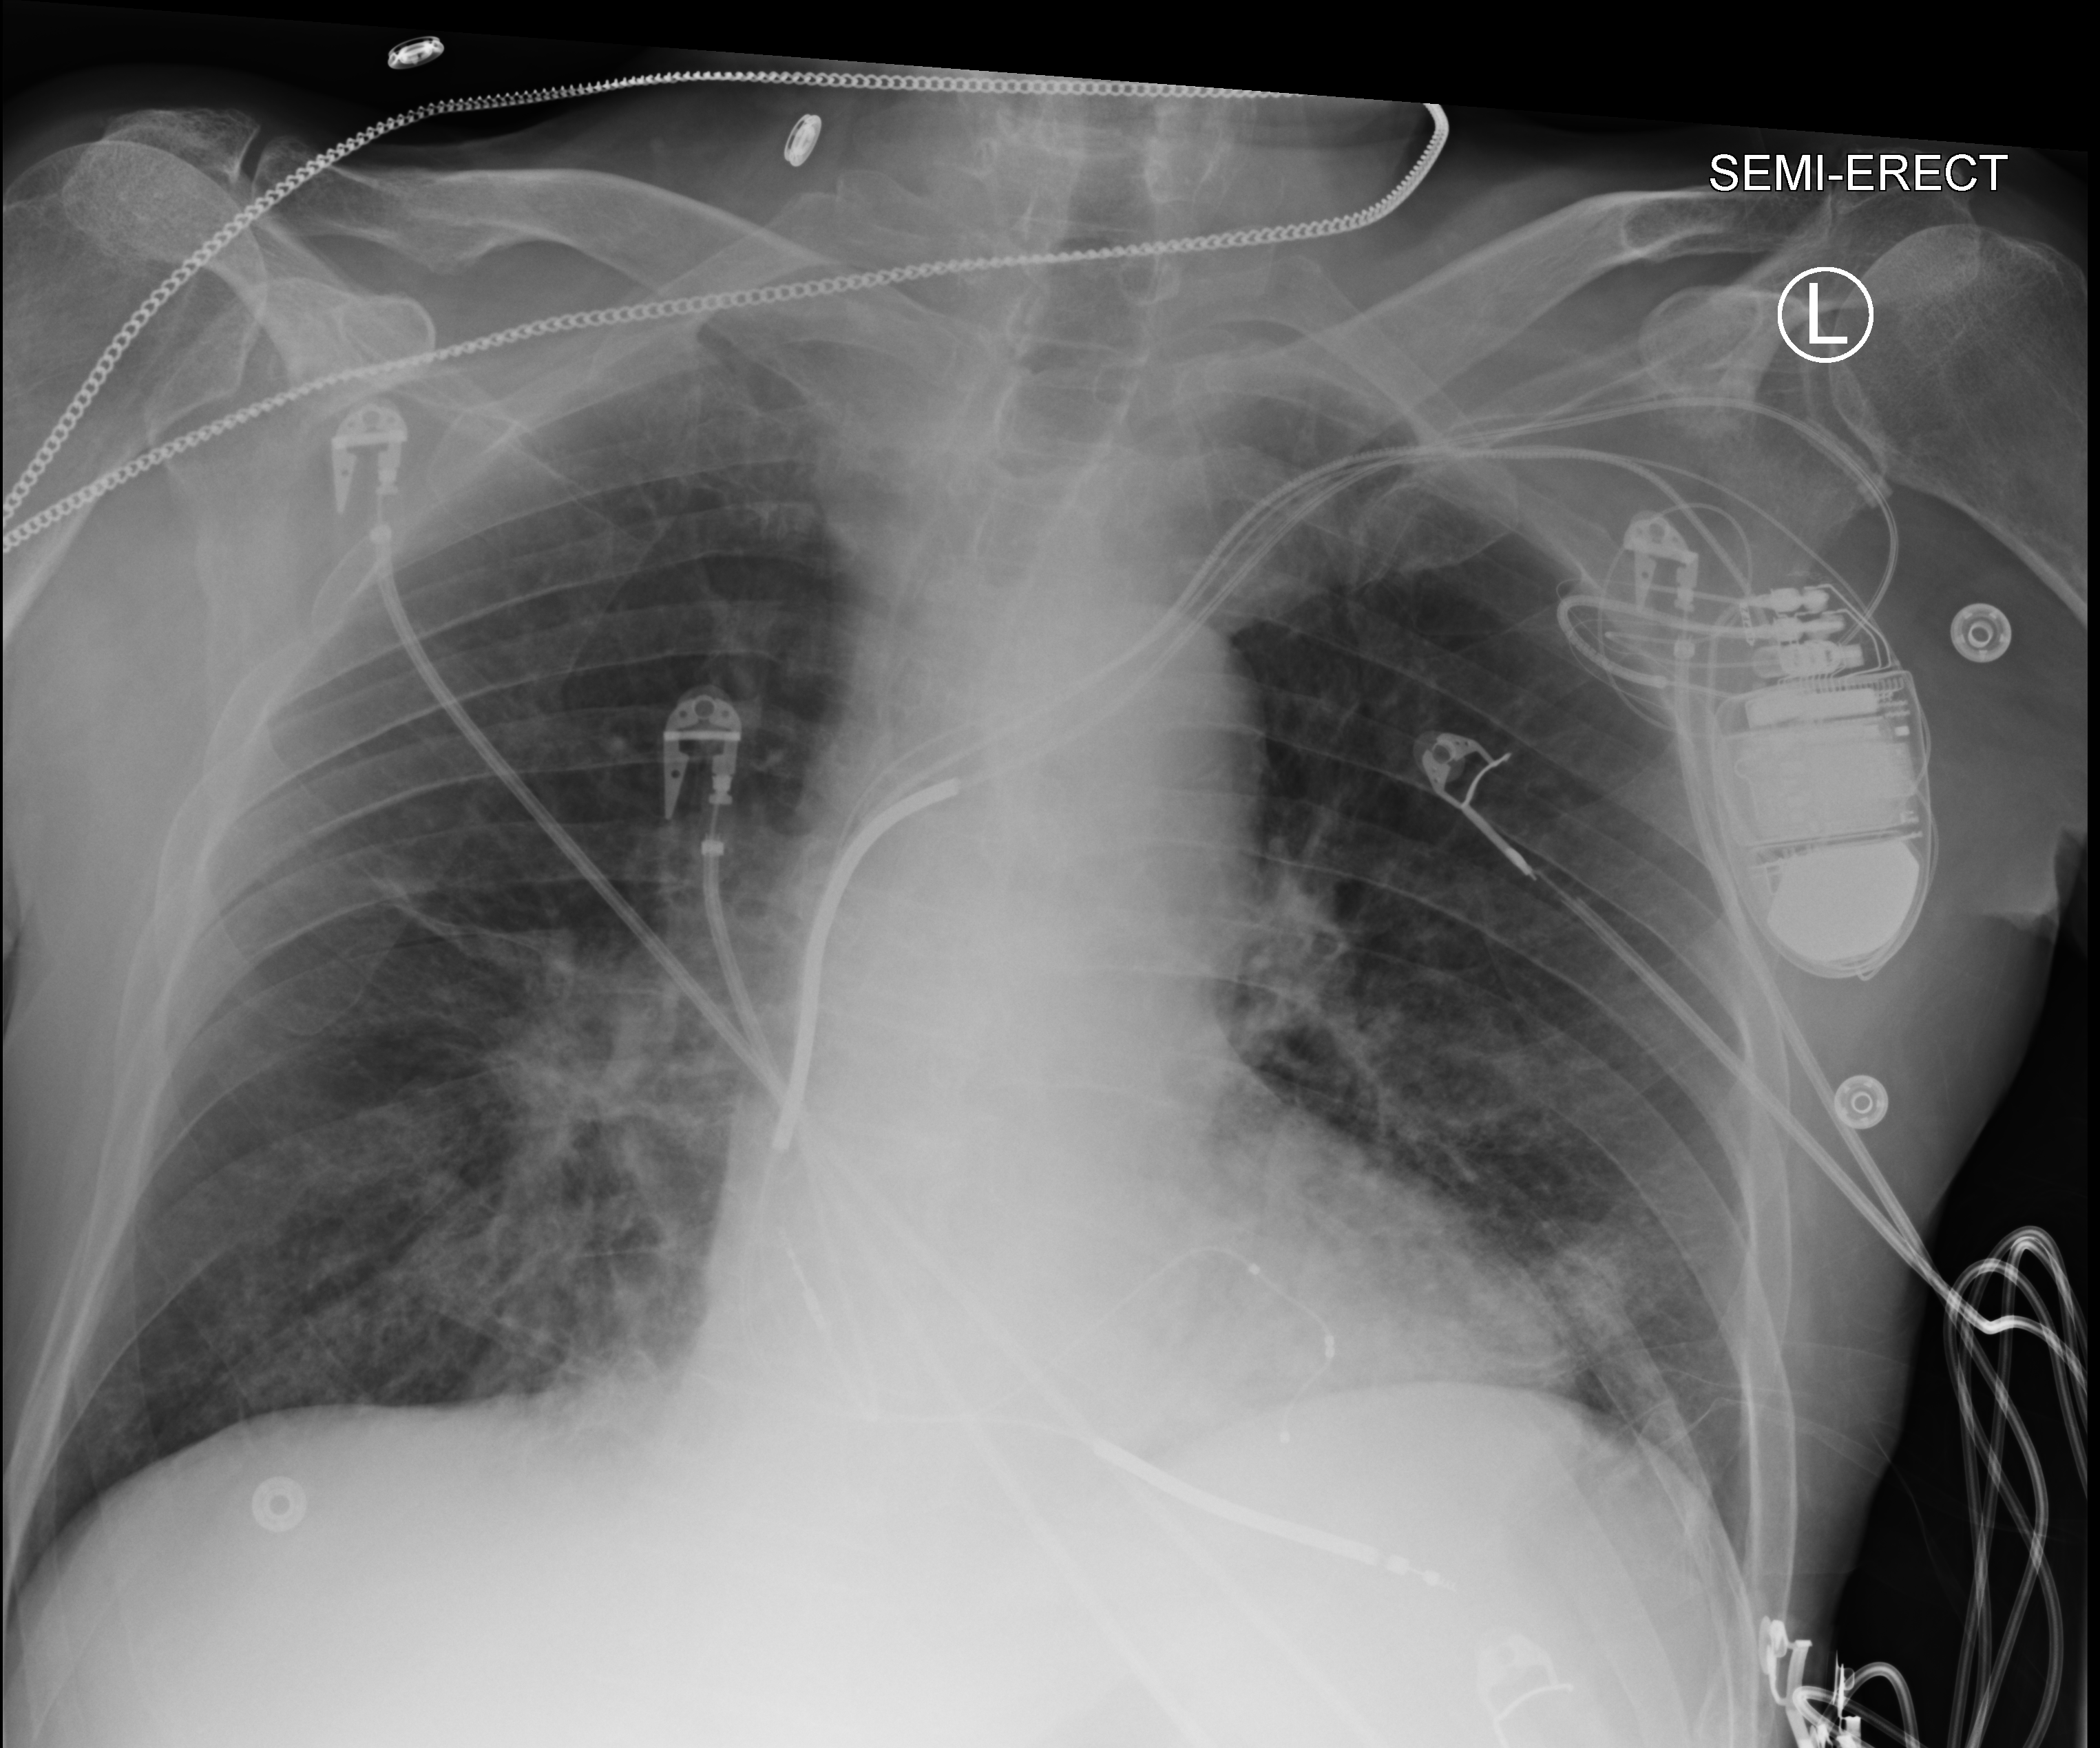
Portable chest radiograph. Male patient hospitalised with COVID-19, age 75–90 years.
From the hospital-stay record, not from the radiograph (when in the stay this image was taken is not recorded): mechanically ventilated during this hospital stay: no.